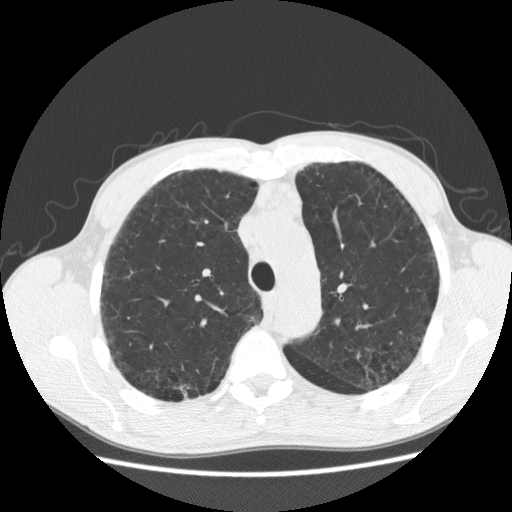
Chest CT (low-dose screening protocol), one axial image; second annual screen; lung window (W 1500 / L -600 HU); slice 141 of 195 in the series; 512 × 512 image matrix, field of view 355 × 355 mm. Male participant, aged 60 years at enrolment.
Expert-annotated lung lesion, bounding box (x1, y1, x2, y2) in pixels: (169, 377, 211, 410). Screening reader's record for this exam (one nodule recorded; not confirmed to be the boxed lesion): non-calcified nodule or mass ≥4 mm, right upper lobe, 8 × 5 mm, poorly defined margins, soft tissue attenuation, pre-existing on the prior screen: yes; interval growth: yes. Later outcome: lung cancer diagnosed 204 days after this screen — squamous cell carcinoma, NOS, right upper lobe, well differentiated (G1), stage IA (AJCC 6th edition), 15 mm at pathology.